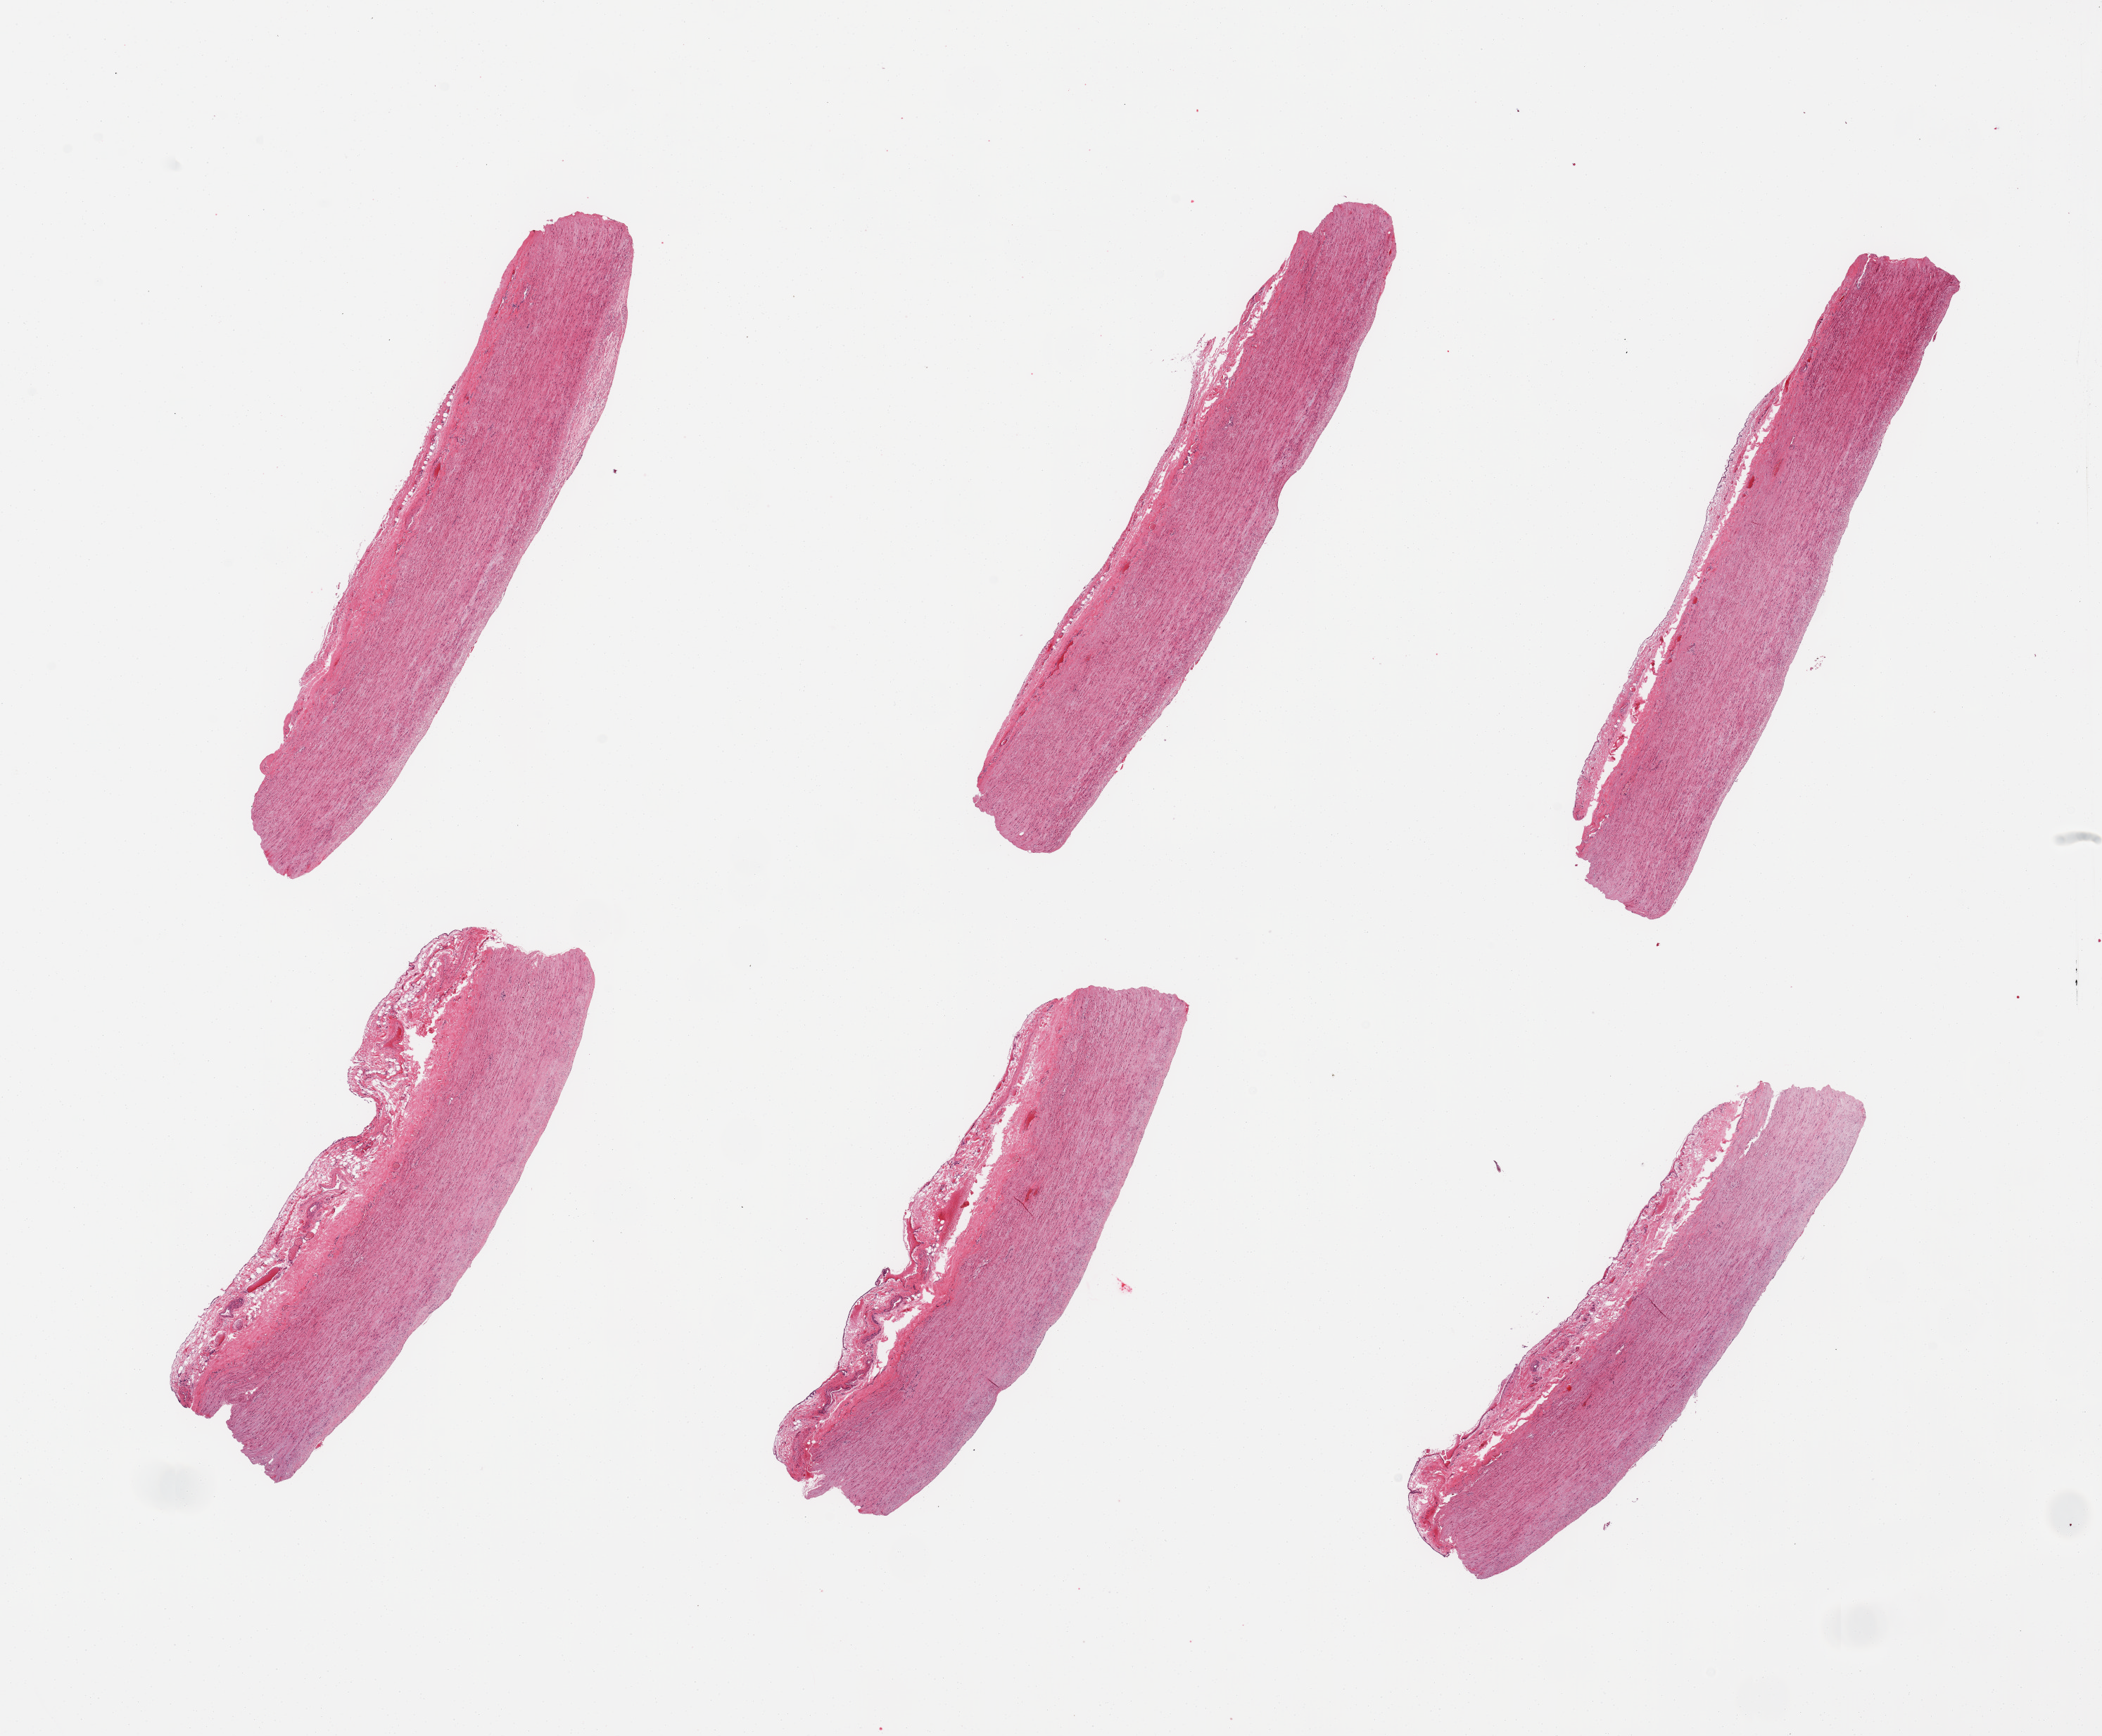
Digitized haematoxylin and eosin-stained section — a low-resolution overview of the entire scanned area, about 23.6 x 19.5 mm; PAXgene-fixed paraffin-embedded (PFPE) section; section of aorta (target tissue); donor tissue sample. Male donor.
Pathologist's review note for this sample: 6 pieces, minimal atherosis.